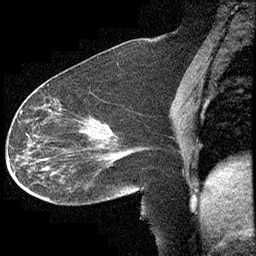
Breast MRI (dynamic contrast-enhanced), one sagittal slice; position 167 of 232 along the scan axis; dynamic contrast-enhanced study with each time point stored as its own series, time point 2 of 4 at this slice position (early post-contrast, ordered by acquisition time); 1.5 T; TE 4.2 ms, TR 6.7 ms; 3 mm slice thickness; 256 × 256 image matrix, field of view 200 × 200 mm. Patient: female, 63 years. Case-level facts recorded for this patient, not image findings: setting: breast cancer imaged before/during neoadjuvant chemotherapy; receptor status: triple-negative.
Annotated regions visible in this slice (semi-automatic segmentation, software-assisted and operator-edited):
- analysis volume of interest (the breast-tissue region the enhancement analysis was run in; not a lesion): bounding box [x1, y1, x2, y2] px = [13, 90, 140, 206]
- tumour enhancement mask (voxels above the 70 % enhancement threshold inside the analysis volume of interest): [20, 111, 43, 170]